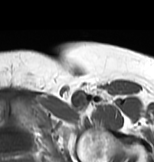
MRI of an extremity soft-tissue mass, one axial slice. Slice 60 of 83 in the series (ordered by position). MR volume resampled by the dataset authors to the PET/CT grid (not the native acquisition matrix). 154 × 162 image matrix, field of view 150 × 158 mm. Female patient. From the clinical record (not read from this slice): histological type: myxofibrosarcoma; grade: intermediate; site of the primary tumour: left thigh.
Annotated regions visible in this slice (expert contour drawn on MRI and transferred to this co-registered scan by the dataset authors):
- gross tumour volume including surrounding oedema: bounding box <62,93,109,113> (left, top, right, bottom; pixels)